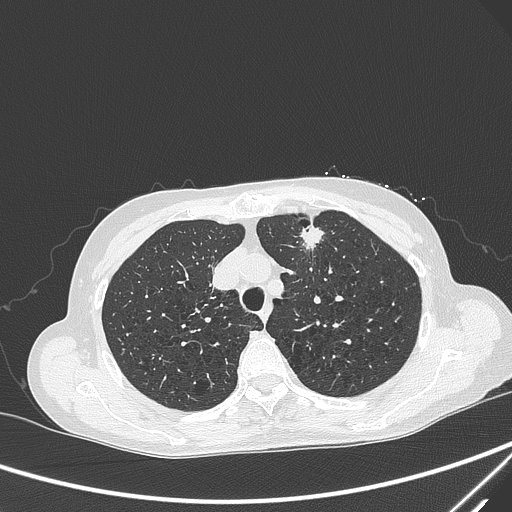
Chest CT, one axial slice. Position 232 of 299 along the scan axis. 120 kVp. Lung window (W 1500 / L -600 HU). 1 mm slice thickness. 512 × 512 image matrix. Female patient, age 71 years. From the clinical record (not read from this slice): clinical TNM (as recorded): T1c N0 M0.
Outlined on this slice (rectangle marked by the reading radiologist):
- lung tumour (recorded histology: adenocarcinoma): bounding box (x1, y1, x2, y2) in pixels: (292, 218, 334, 254)